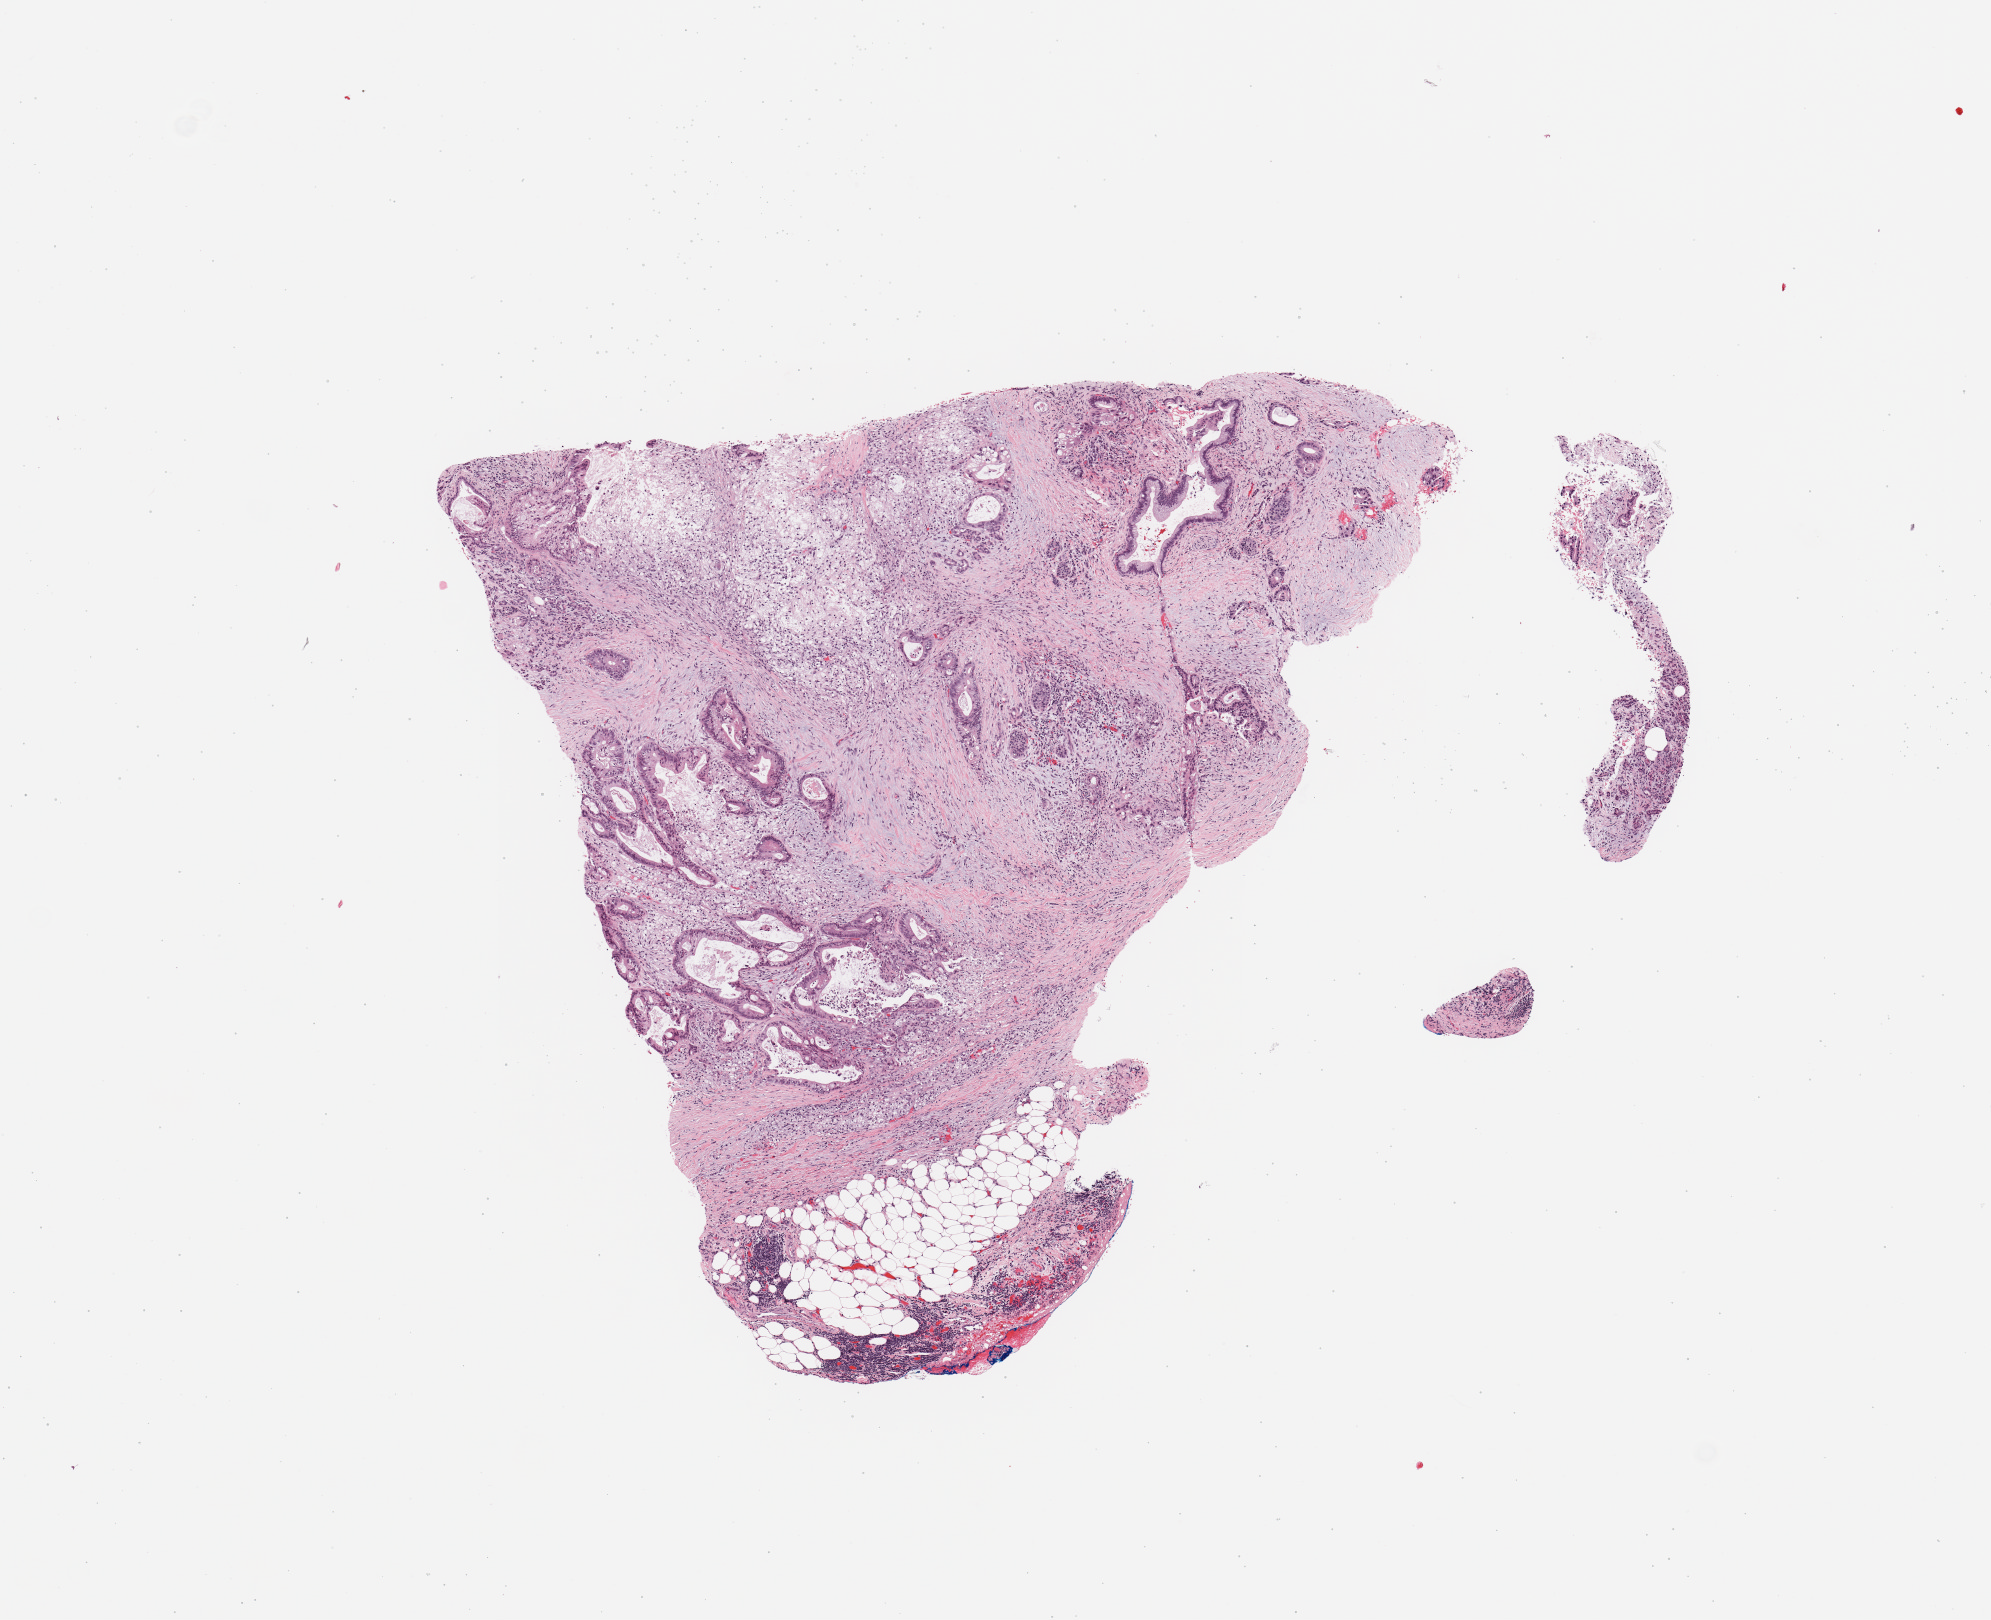
Whole-slide histology image, H&E — shown as a low-resolution overview of the whole scanned area (about 7.9 x 6.4 mm, from a 20x scan); tumour tissue sample, pancreas. 78-year-old female patient.
Histologic diagnosis: Infiltrating duct carcinoma, NOS.